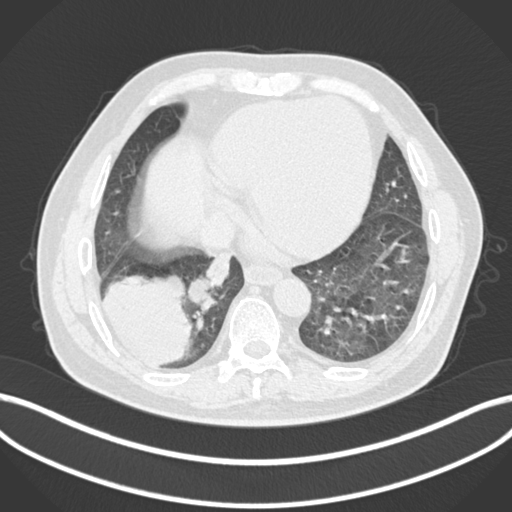
Chest CT, one axial slice. Position 43 of 200 along the scan axis. Reconstruction kernel B30f. 120 kVp. Lung window (W 1500 / L -600 HU). 1 mm slice thickness. 512 × 512 image matrix, field of view 400 × 400 mm. Male patient, age 59 years.
Annotated regions visible in this slice (bounding box drawn by a radiologist):
- lung tumour (recorded histology: adenocarcinoma): bounding box <100,274,193,368> (left, top, right, bottom; pixels)